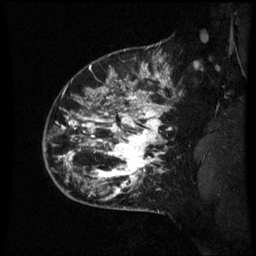
Breast MRI (dynamic contrast-enhanced), one sagittal slice. Slice 51 of 60 in the series (ordered by position). Dynamic contrast-enhanced series, image 2 of 3 at this slice position (ordered by acquisition). 1.5 T. TE 4.2 ms, TR 8.9 ms. 2.1 mm slice thickness. 256 × 256 image matrix. Patient: female, 42 years. From the clinical record (not read from this slice): setting: breast cancer imaged before/during neoadjuvant chemotherapy; receptor status: HER2-positive.
Structures marked on this image (semi-automatic segmentation, software-assisted and operator-edited):
- analysis volume of interest (the breast-tissue region the enhancement analysis was run in; not a lesion): bounding box <66,82,171,193> (left, top, right, bottom; pixels)
- tumour enhancement mask (voxels above the 70 % enhancement threshold inside the analysis volume of interest): <66,82,169,193>